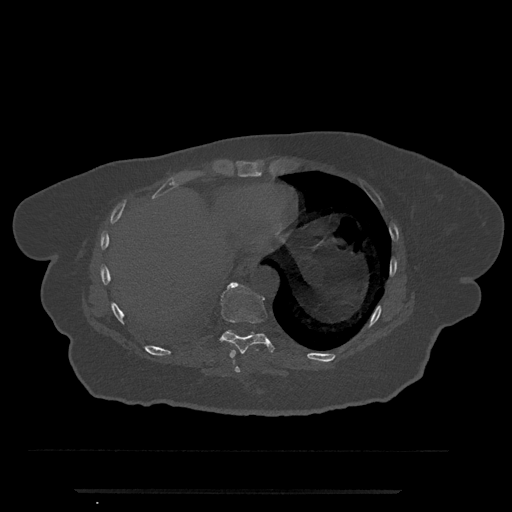
CT including the spine, one axial slice. Position 332 of 797 along the scan axis. Bone window (W 1800 / L 400 HU). 0.5 mm slice thickness. 512 × 512 image matrix, field of view 440 × 440 mm. Female patient, age 51 years. From the clinical record (not read from this slice): primary cancer: neuro.
Outlined on this slice (semi-automatic segmentation, software-assisted and operator-edited):
- T8 vertebra: bounding box [x1, y1, x2, y2] px = [234, 364, 240, 373]
- T9 vertebra: [209, 282, 275, 358]